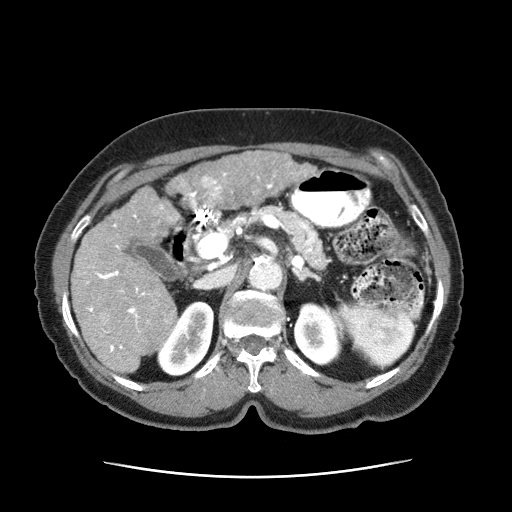
Contrast-enhanced abdominal CT (liver protocol), one axial slice; slice 27 of 63 in the series (ordered by position); reconstruction kernel STANDARD; soft-tissue window (W 400 / L 40 HU); 2.5 mm slice thickness; 512 × 512 image matrix. Female patient, age 79 years. Case-level facts recorded for this patient, not image findings: diagnosis: hepatocellular carcinoma (patient treated with transarterial chemoembolisation; whether this scan precedes or follows treatment is not stated here); TNM stage (as recorded): Stage-II; Child-Pugh class: B; tumour differentiation: well differentiated; tumour size: 5 cm.
Structures marked on this image (semi-automatic segmentation, software-assisted and operator-edited):
- abdominal aorta: bounding box [x1, y1, x2, y2] px = [249, 254, 281, 291]
- liver parenchyma outside the tumour (the mass and vessels are separate outlines, so this box may not span the whole liver): [71, 185, 185, 376]
- mass: [167, 152, 317, 206]
- liver vessels: [83, 173, 227, 353]